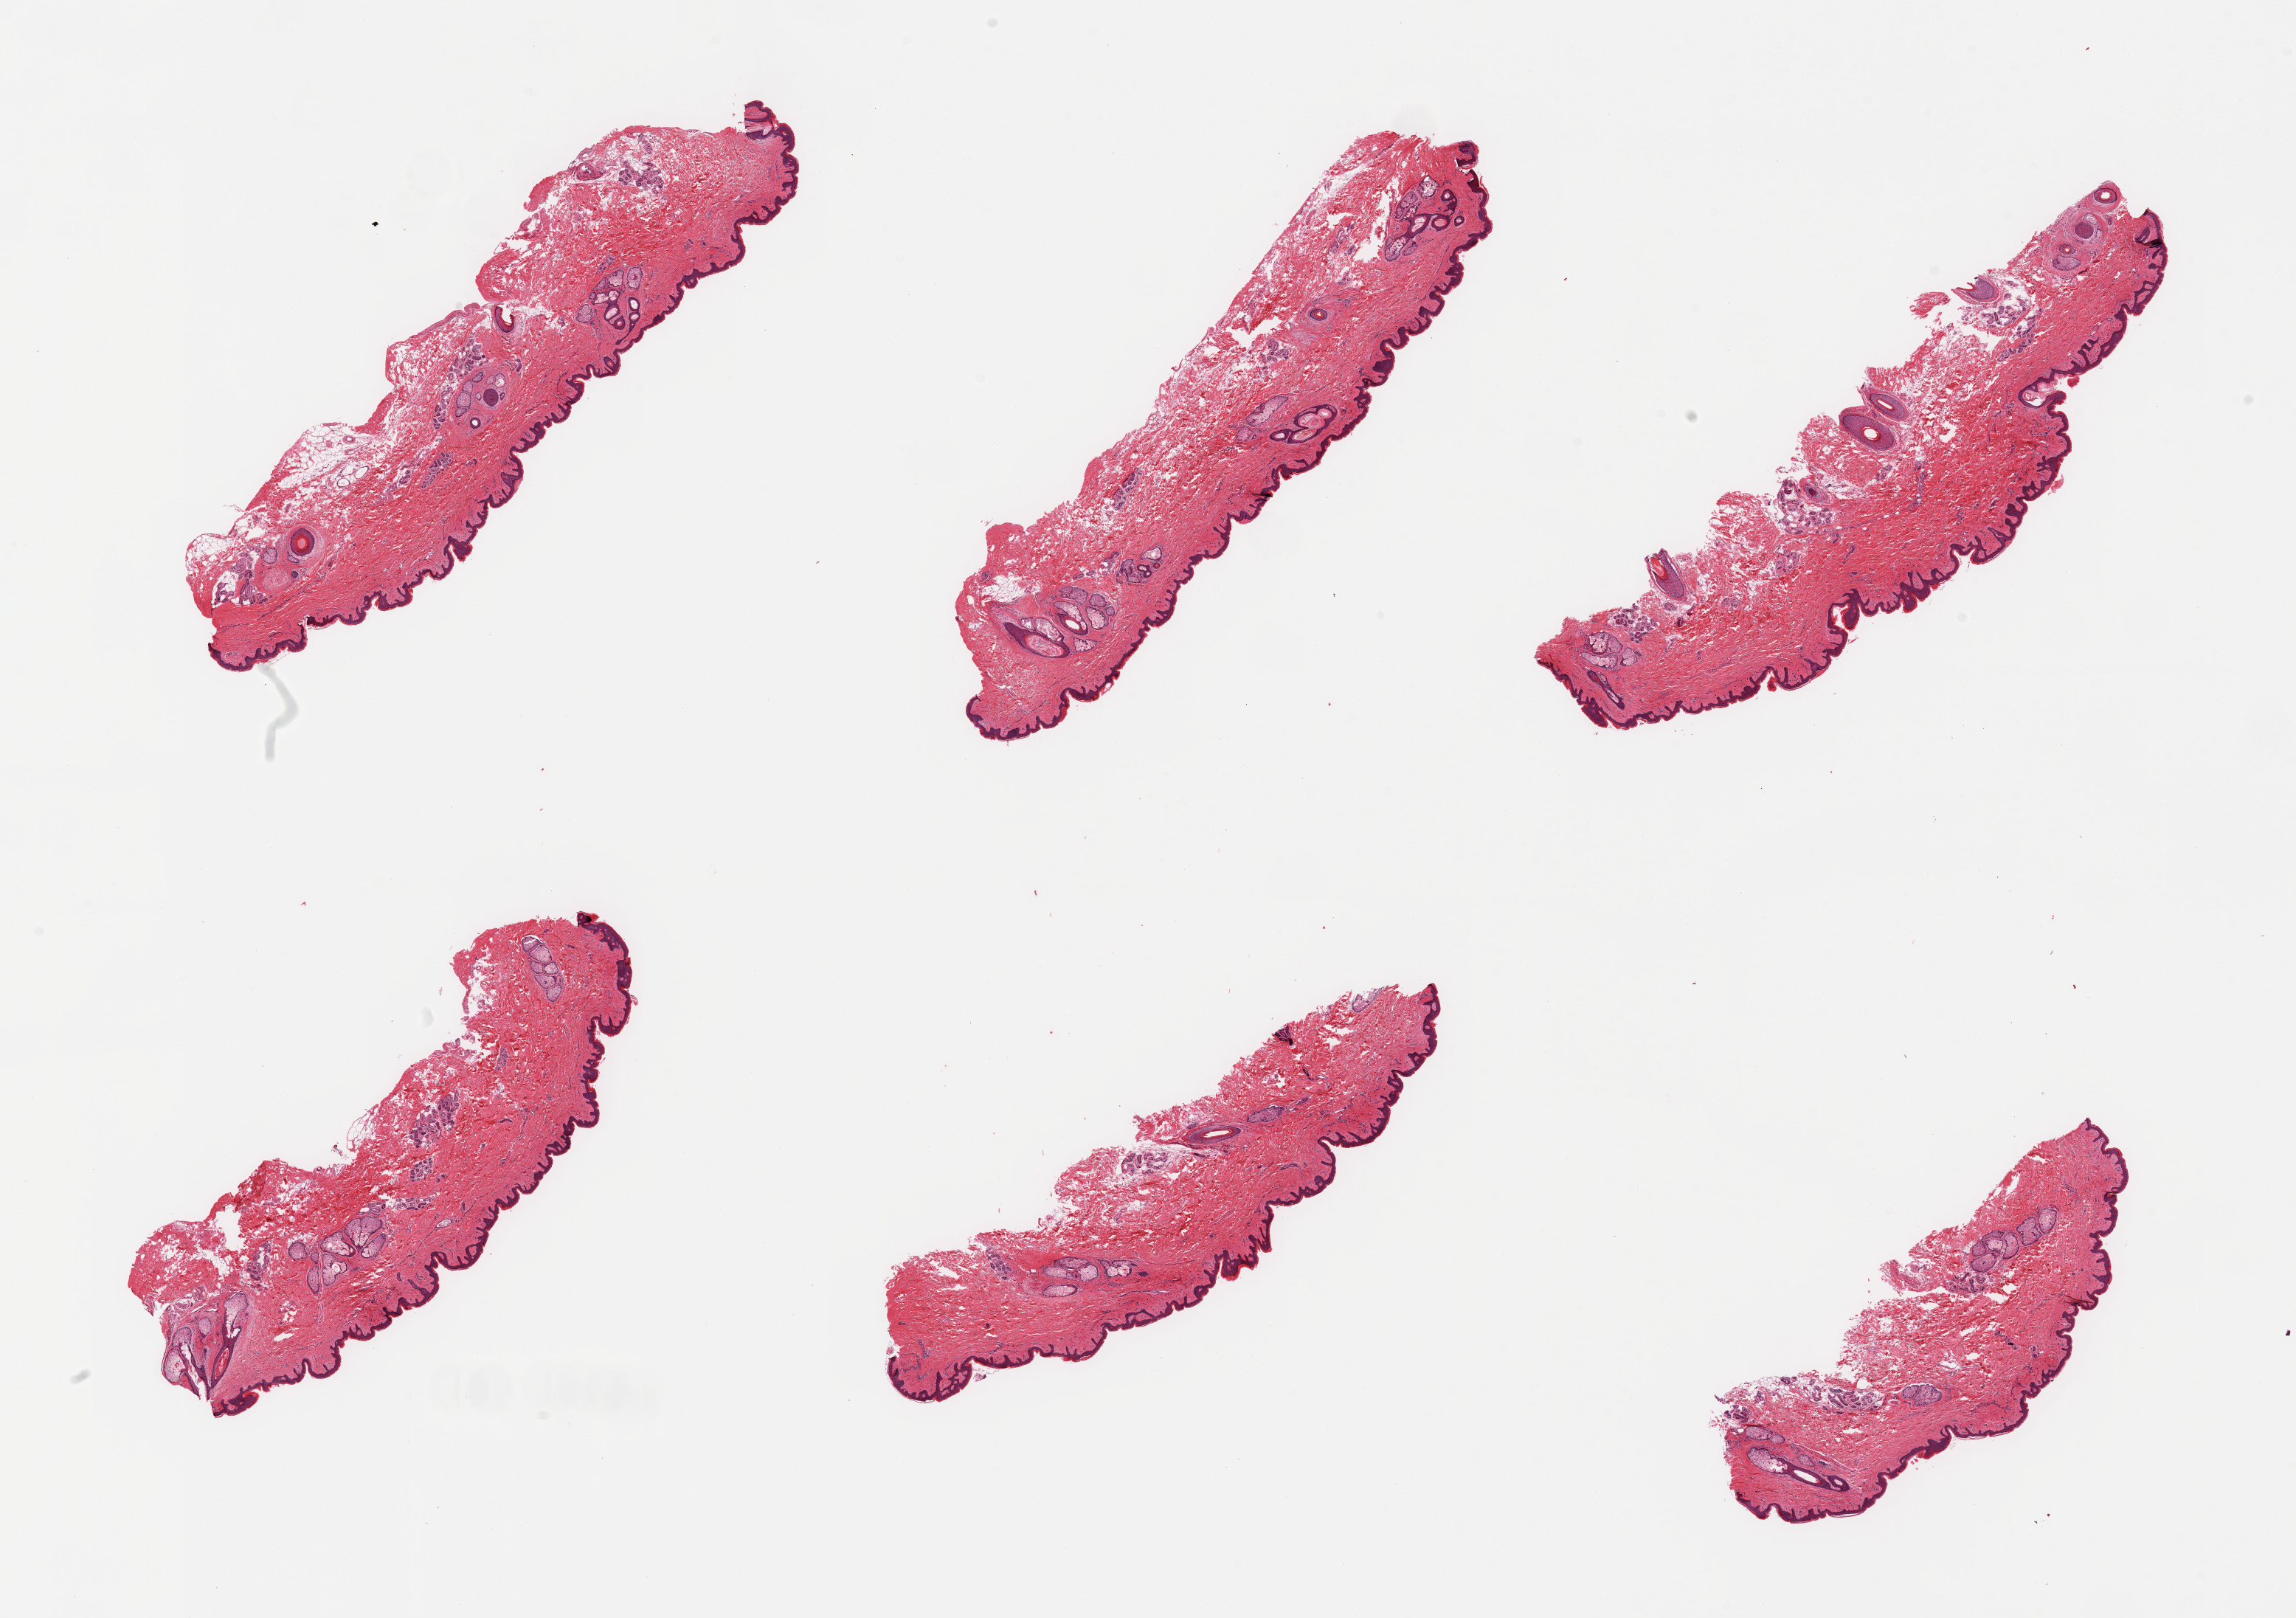
Haematoxylin and eosin whole-slide image, whole scanned area (about 24.6 x 17.3 mm) shown as a low-resolution overview. PAXgene-fixed, paraffin-embedded tissue. Section of skin of suprapubic region (target tissue). Donor tissue sample.
• pathologist's review note for this sample: 6 pieces; well trimmed; 5% dermal fat